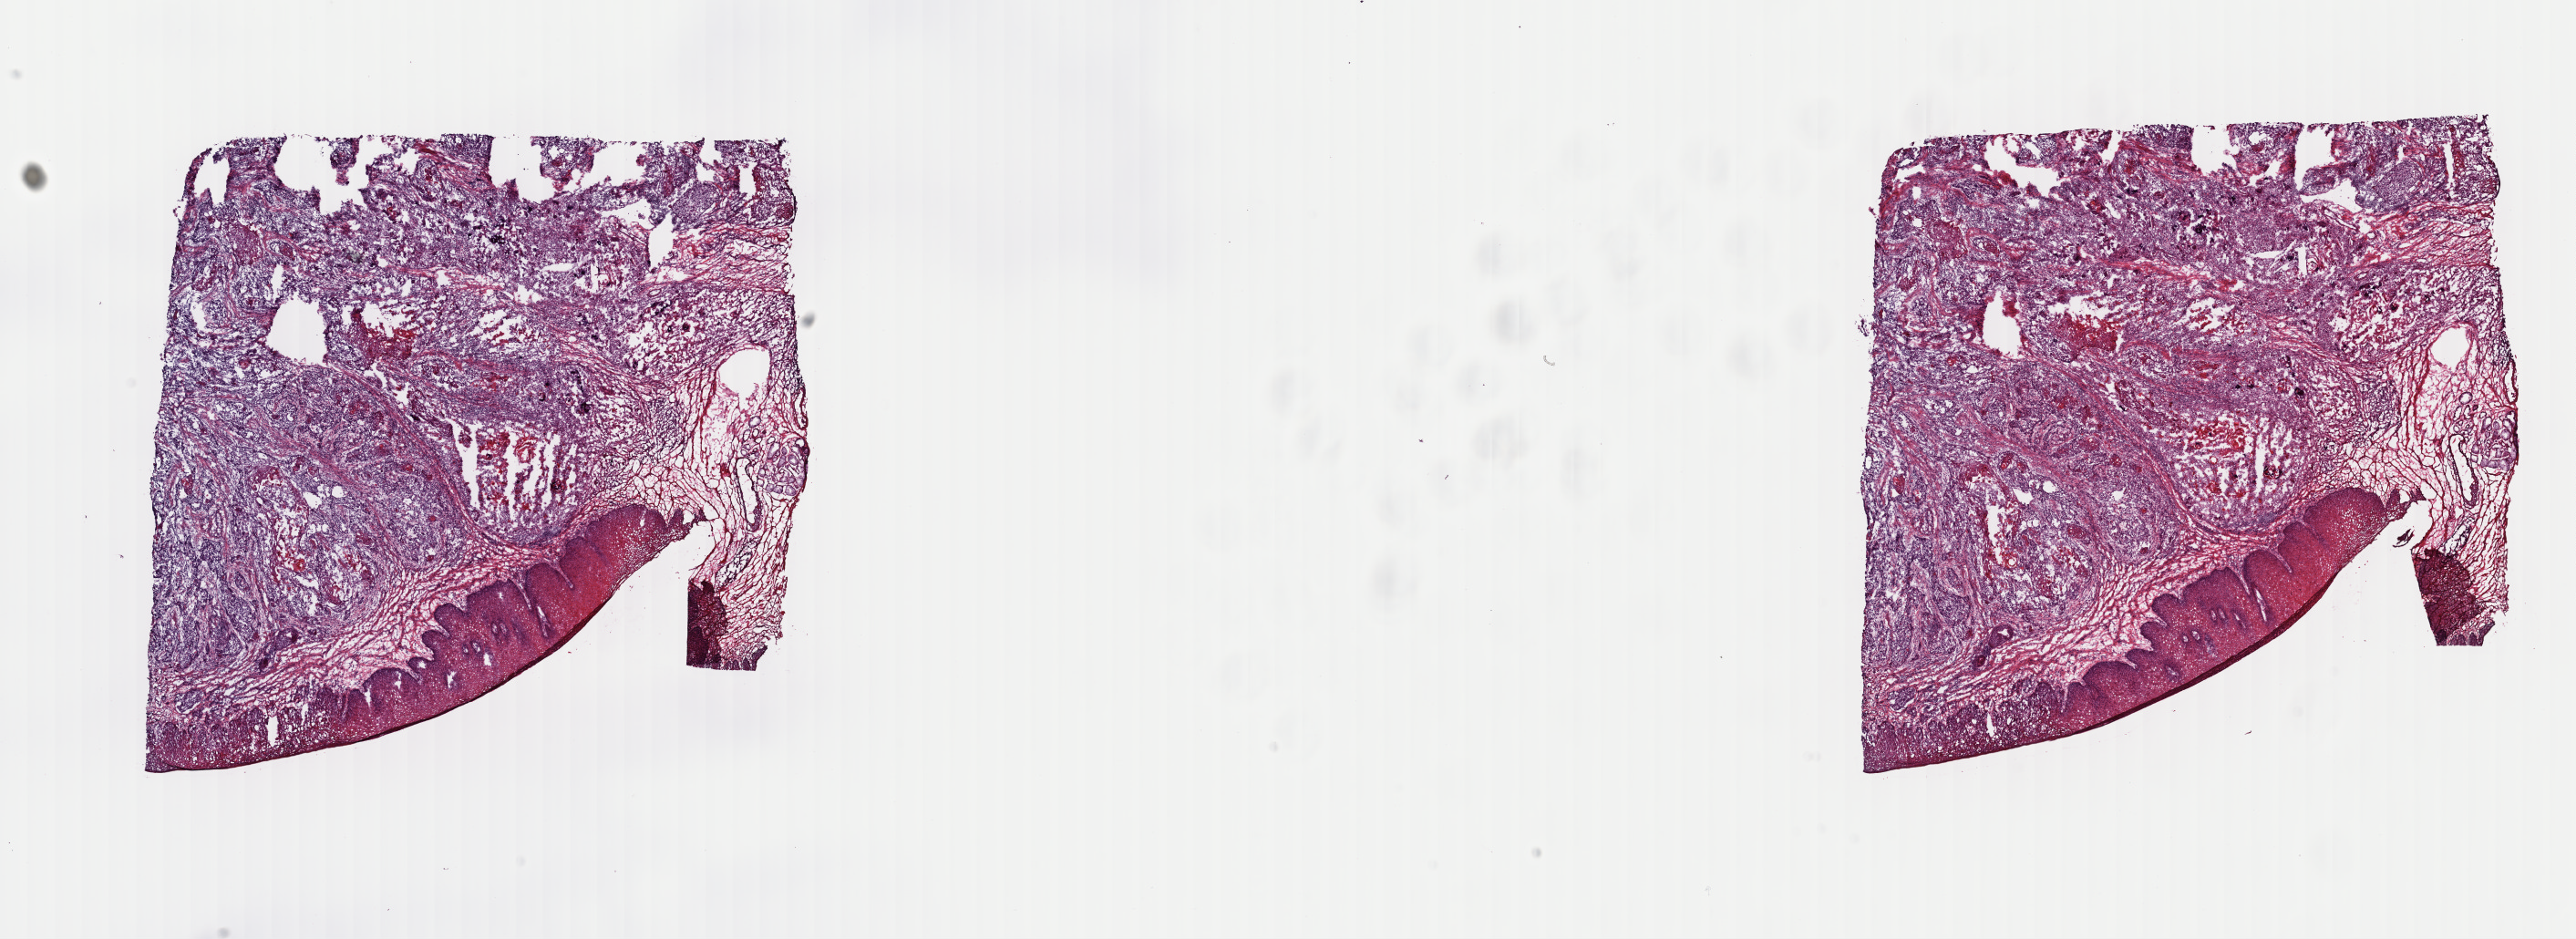
Digitized H&E tissue section (whole slide), whole scanned area (about 22.3 x 8.1 mm, acquisition: 40x scan) shown as a low-resolution overview; frozen section from the top of the tissue portion; sample: primary tumour, esophagus. Male patient; age at initial diagnosis 62 years. Histologic grade: G2 (moderately differentiated). Composition of this section per pathologist review: tumour cells 59%, tumour nuclei 85%, normal cells 15%, stromal cells 25%, necrosis 1%. Inflammatory infiltration, as recorded: lymphocyte infiltration 3%, monocyte infiltration 2%, neutrophil infiltration 1%.
Diagnosis: Squamous cell carcinoma, NOS (lower third of esophagus). AJCC pathologic stage: IIIA (7th edition). Lymph nodes positive (case pathology): 1 of 5 examined.